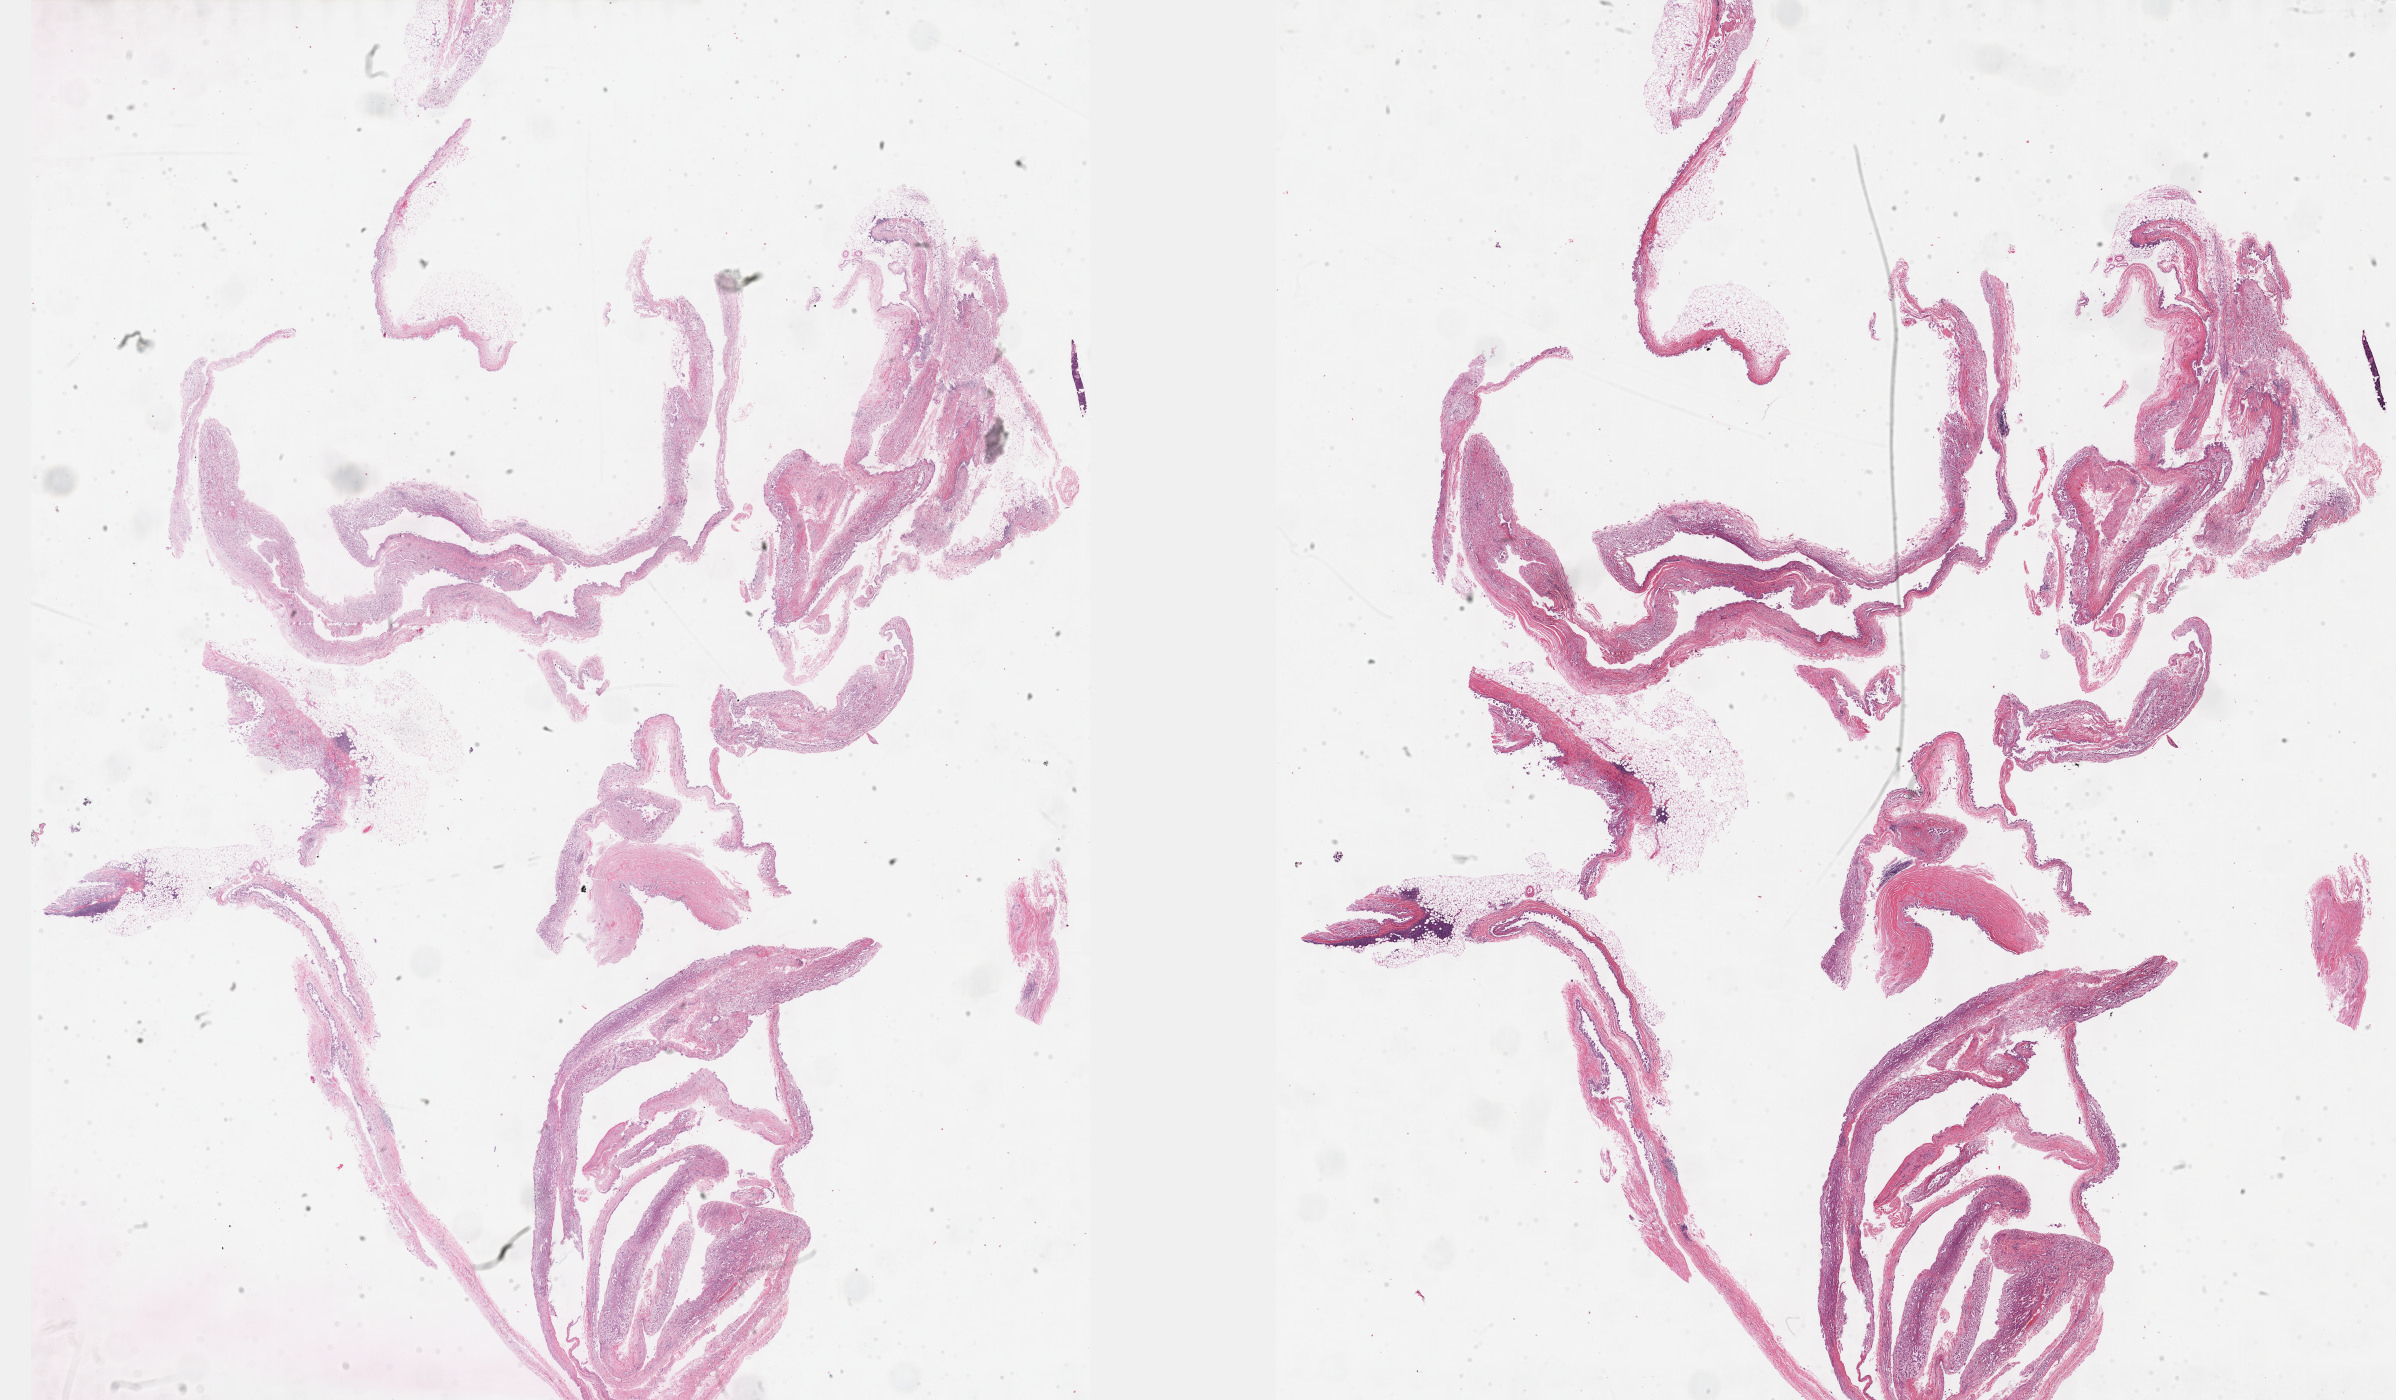
Whole-slide histology image, H&E, a low-resolution overview of the entire scanned area, about 38.7 x 22.6 mm; formalin-fixed paraffin-embedded (FFPE) diagnostic section; primary tumour sample from the mesothelium. Male, age 62 years at initial diagnosis.
AJCC pathologic stage: III (7th edition). Pathologic diagnosis: Epithelioid mesothelioma, malignant (pleura, NOS). TNM: T3 N2 M0. Laterality: right.